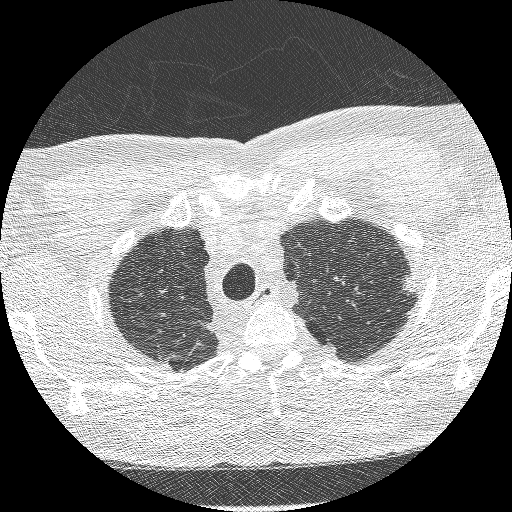
Chest CT (low-dose screening protocol), one axial image; third screening round (two years after baseline); lung window (W 1500 / L -600 HU); 1.25 mm slice thickness; 512 × 512 image matrix. Male, age 66 years at enrolment. Current smoker at enrolment.
• Expert-annotated lung lesion, bounding box <386,269,431,316> (left, top, right, bottom; pixels).
• The exam's reader record, not a measurement of the box and not confirmed to be the same lesion: non-calcified nodule or mass ≥4 mm, left lower lobe, 15 × 9 mm, spiculated (stellate) margins, soft tissue attenuation, pre-existing on the prior screen: yes; interval growth: yes.
• Lung cancer was diagnosed 225 days after this screen: adenocarcinoma, NOS, left upper lobe, poorly differentiated (G3), stage IB (AJCC 6th edition), 16 mm at pathology.